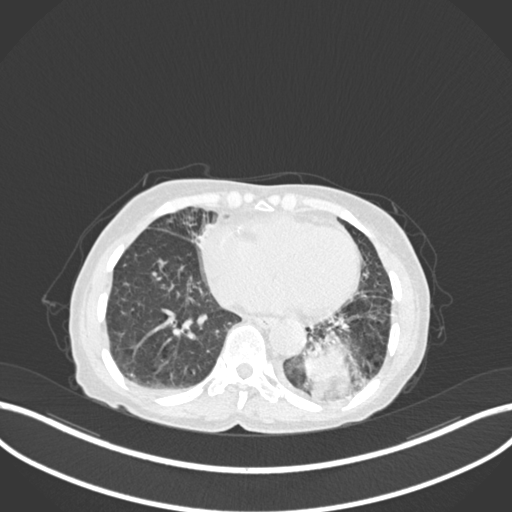
Chest CT, one axial slice. Position 38 of 233 along the scan axis. Reconstruction kernel B30f. Lung window (W 1500 / L -600 HU). 512 × 512 image matrix, field of view 400 × 400 mm. Patient: female, 78 years. Case-level facts recorded for this patient, not image findings: clinical TNM (as recorded): T3 N0 M1.
Structures marked on this image (rectangle marked by the reading radiologist):
- lung tumour (recorded histology: squamous cell carcinoma): bounding box [x1, y1, x2, y2] px = [300, 330, 365, 400]